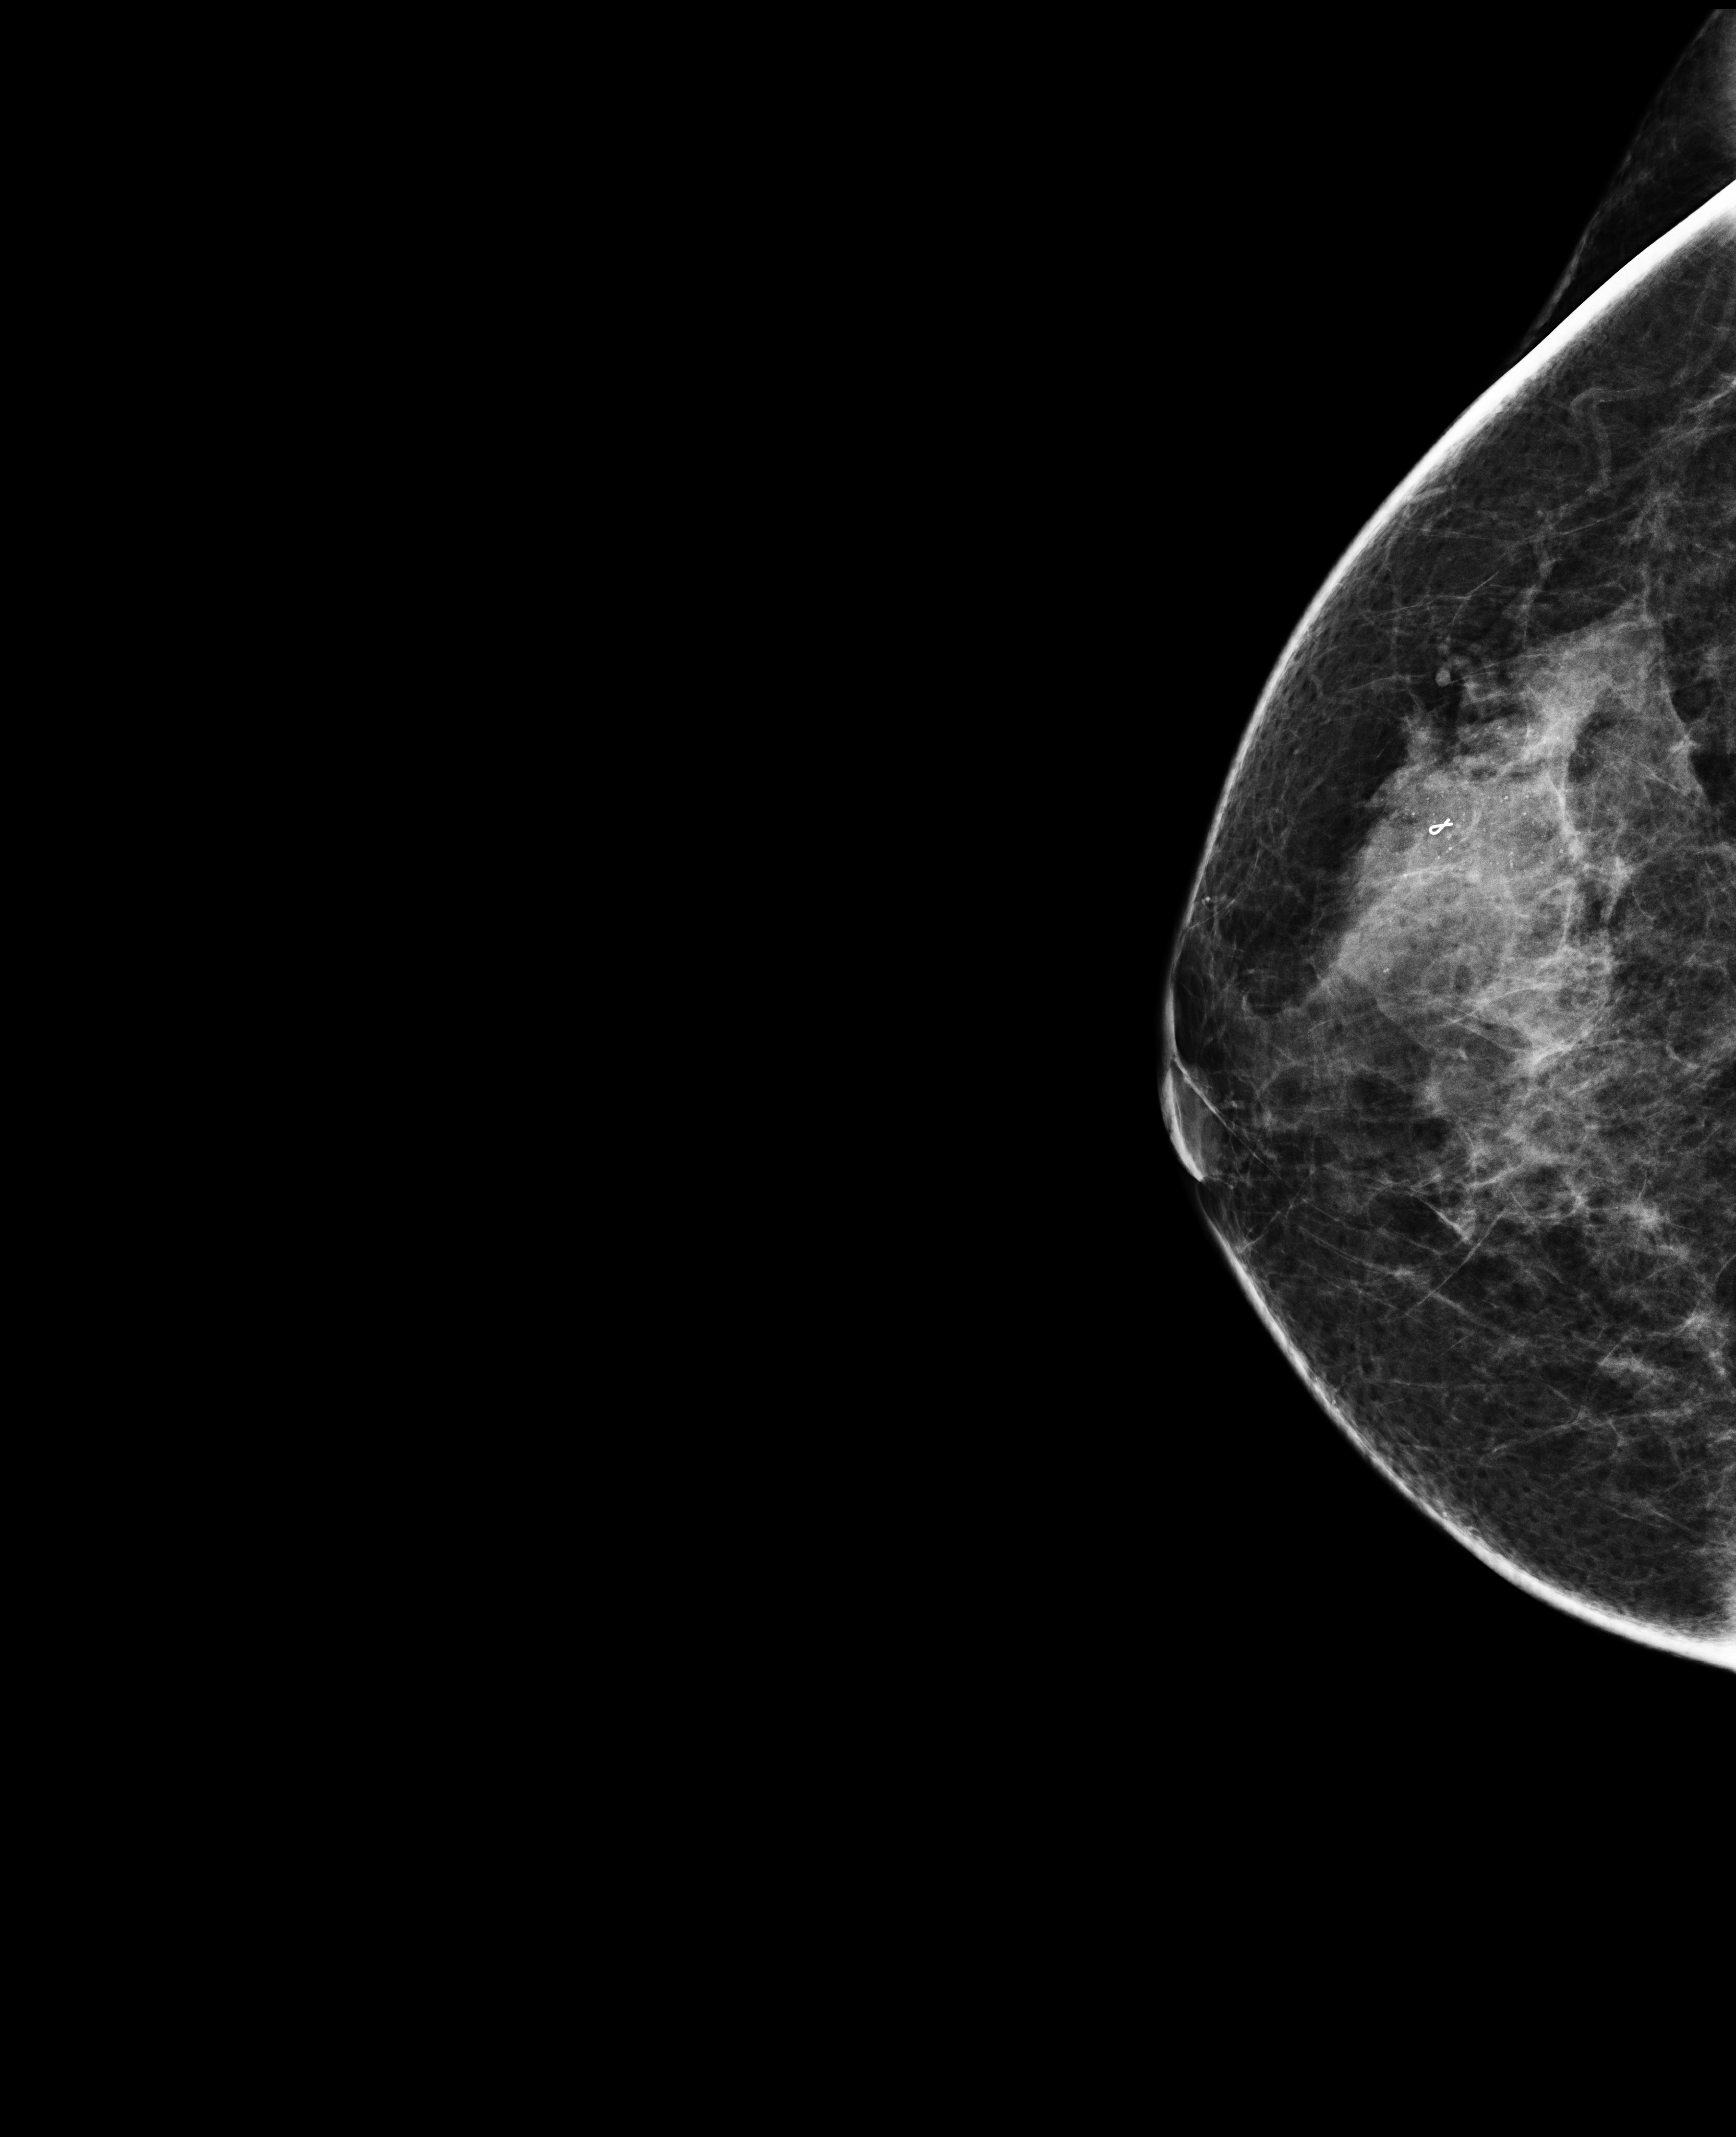
Screening examination, compressed breast thickness 72 mm, system: Selenia Dimensions. Patient aged 49 years (female).
Image type: full-field digital mammogram. Breast: right. Projection: craniocaudal (CC) view.